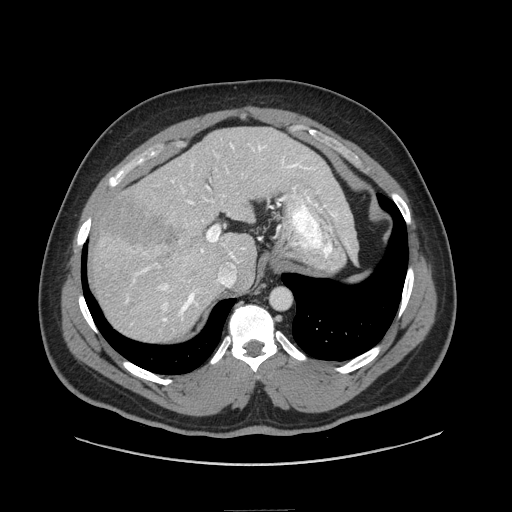
Contrast-enhanced abdominal CT (liver protocol), one axial slice. Slice 57 of 87 in the series (ordered by position). Reconstruction kernel STANDARD. 140 kVp. Soft-tissue window (W 400 / L 40 HU). 2.5 mm slice thickness. 512 × 512 image matrix. Case-level facts recorded for this patient, not image findings: diagnosis: hepatocellular carcinoma (patient treated with transarterial chemoembolisation; whether this scan precedes or follows treatment is not stated here); TNM stage (as recorded): Stage-II; Child-Pugh class: A; tumour differentiation: moderately differentiated; tumour nodularity: uninodular.
Outlined on this slice (semi-automatically segmented with operator editing):
- liver parenchyma outside the tumour (the mass and vessels are separate outlines, so this box may not span the whole liver): bounding box <88,126,345,340> (left, top, right, bottom; pixels)
- mass: <99,193,179,254>
- liver vessels: <126,143,326,322>